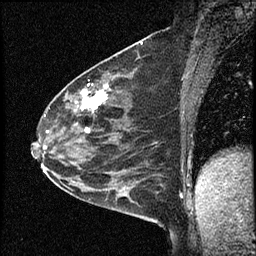
Breast MRI (dynamic contrast-enhanced), one sagittal slice; slice 35 of 60 in the series (ordered by position); dynamic contrast-enhanced study with each time point stored as its own series, time point 2 of 4 at this slice position (early post-contrast, ordered by acquisition time); 1.5 T; TE 4.2 ms, TR 17.6 ms; 2 mm slice thickness; 256 × 256 image matrix. Patient: female, 53 years. Case-level facts recorded for this patient, not image findings: setting: breast cancer imaged before/during neoadjuvant chemotherapy; receptor status: HR-positive, HER2-negative.
Annotated regions visible in this slice (semi-automatically segmented with operator editing):
- analysis volume of interest (the breast-tissue region the enhancement analysis was run in; not a lesion): box from (x=42, y=69) to (x=156, y=199) px
- tumour enhancement mask (voxels above the 100 % enhancement threshold inside the analysis volume of interest): (x=75, y=84)–(x=108, y=133)